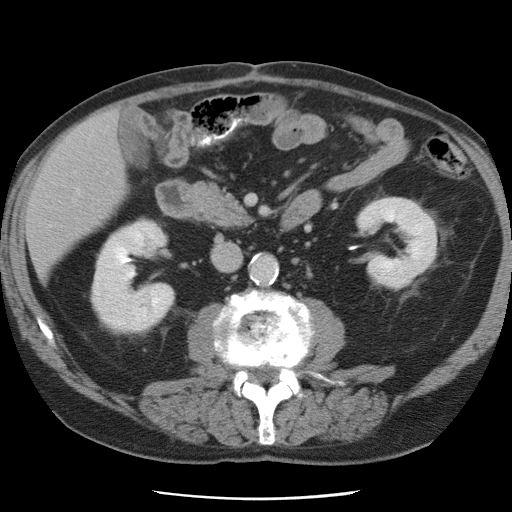
Contrast-enhanced abdominal CT, one axial slice; position 24 of 78 along the scan axis; 120 kVp; intravenous contrast given; soft-tissue window (W 400 / L 40 HU); 512 × 512 image matrix, field of view 337 × 337 mm. Male patient, age 75 years. From the clinical record (not read from this slice): diagnosis: colorectal cancer liver metastases, imaged before liver resection; multiple liver metastases: yes; largest metastasis: 2.4 cm; chemotherapy before resection: yes.
Outlined on this slice (expert manual segmentation):
- liver: bounding box (x1, y1, x2, y2) in pixels: (28, 113, 127, 277)
- planned liver remnant (the part of the liver to remain after resection): (28, 119, 127, 277)